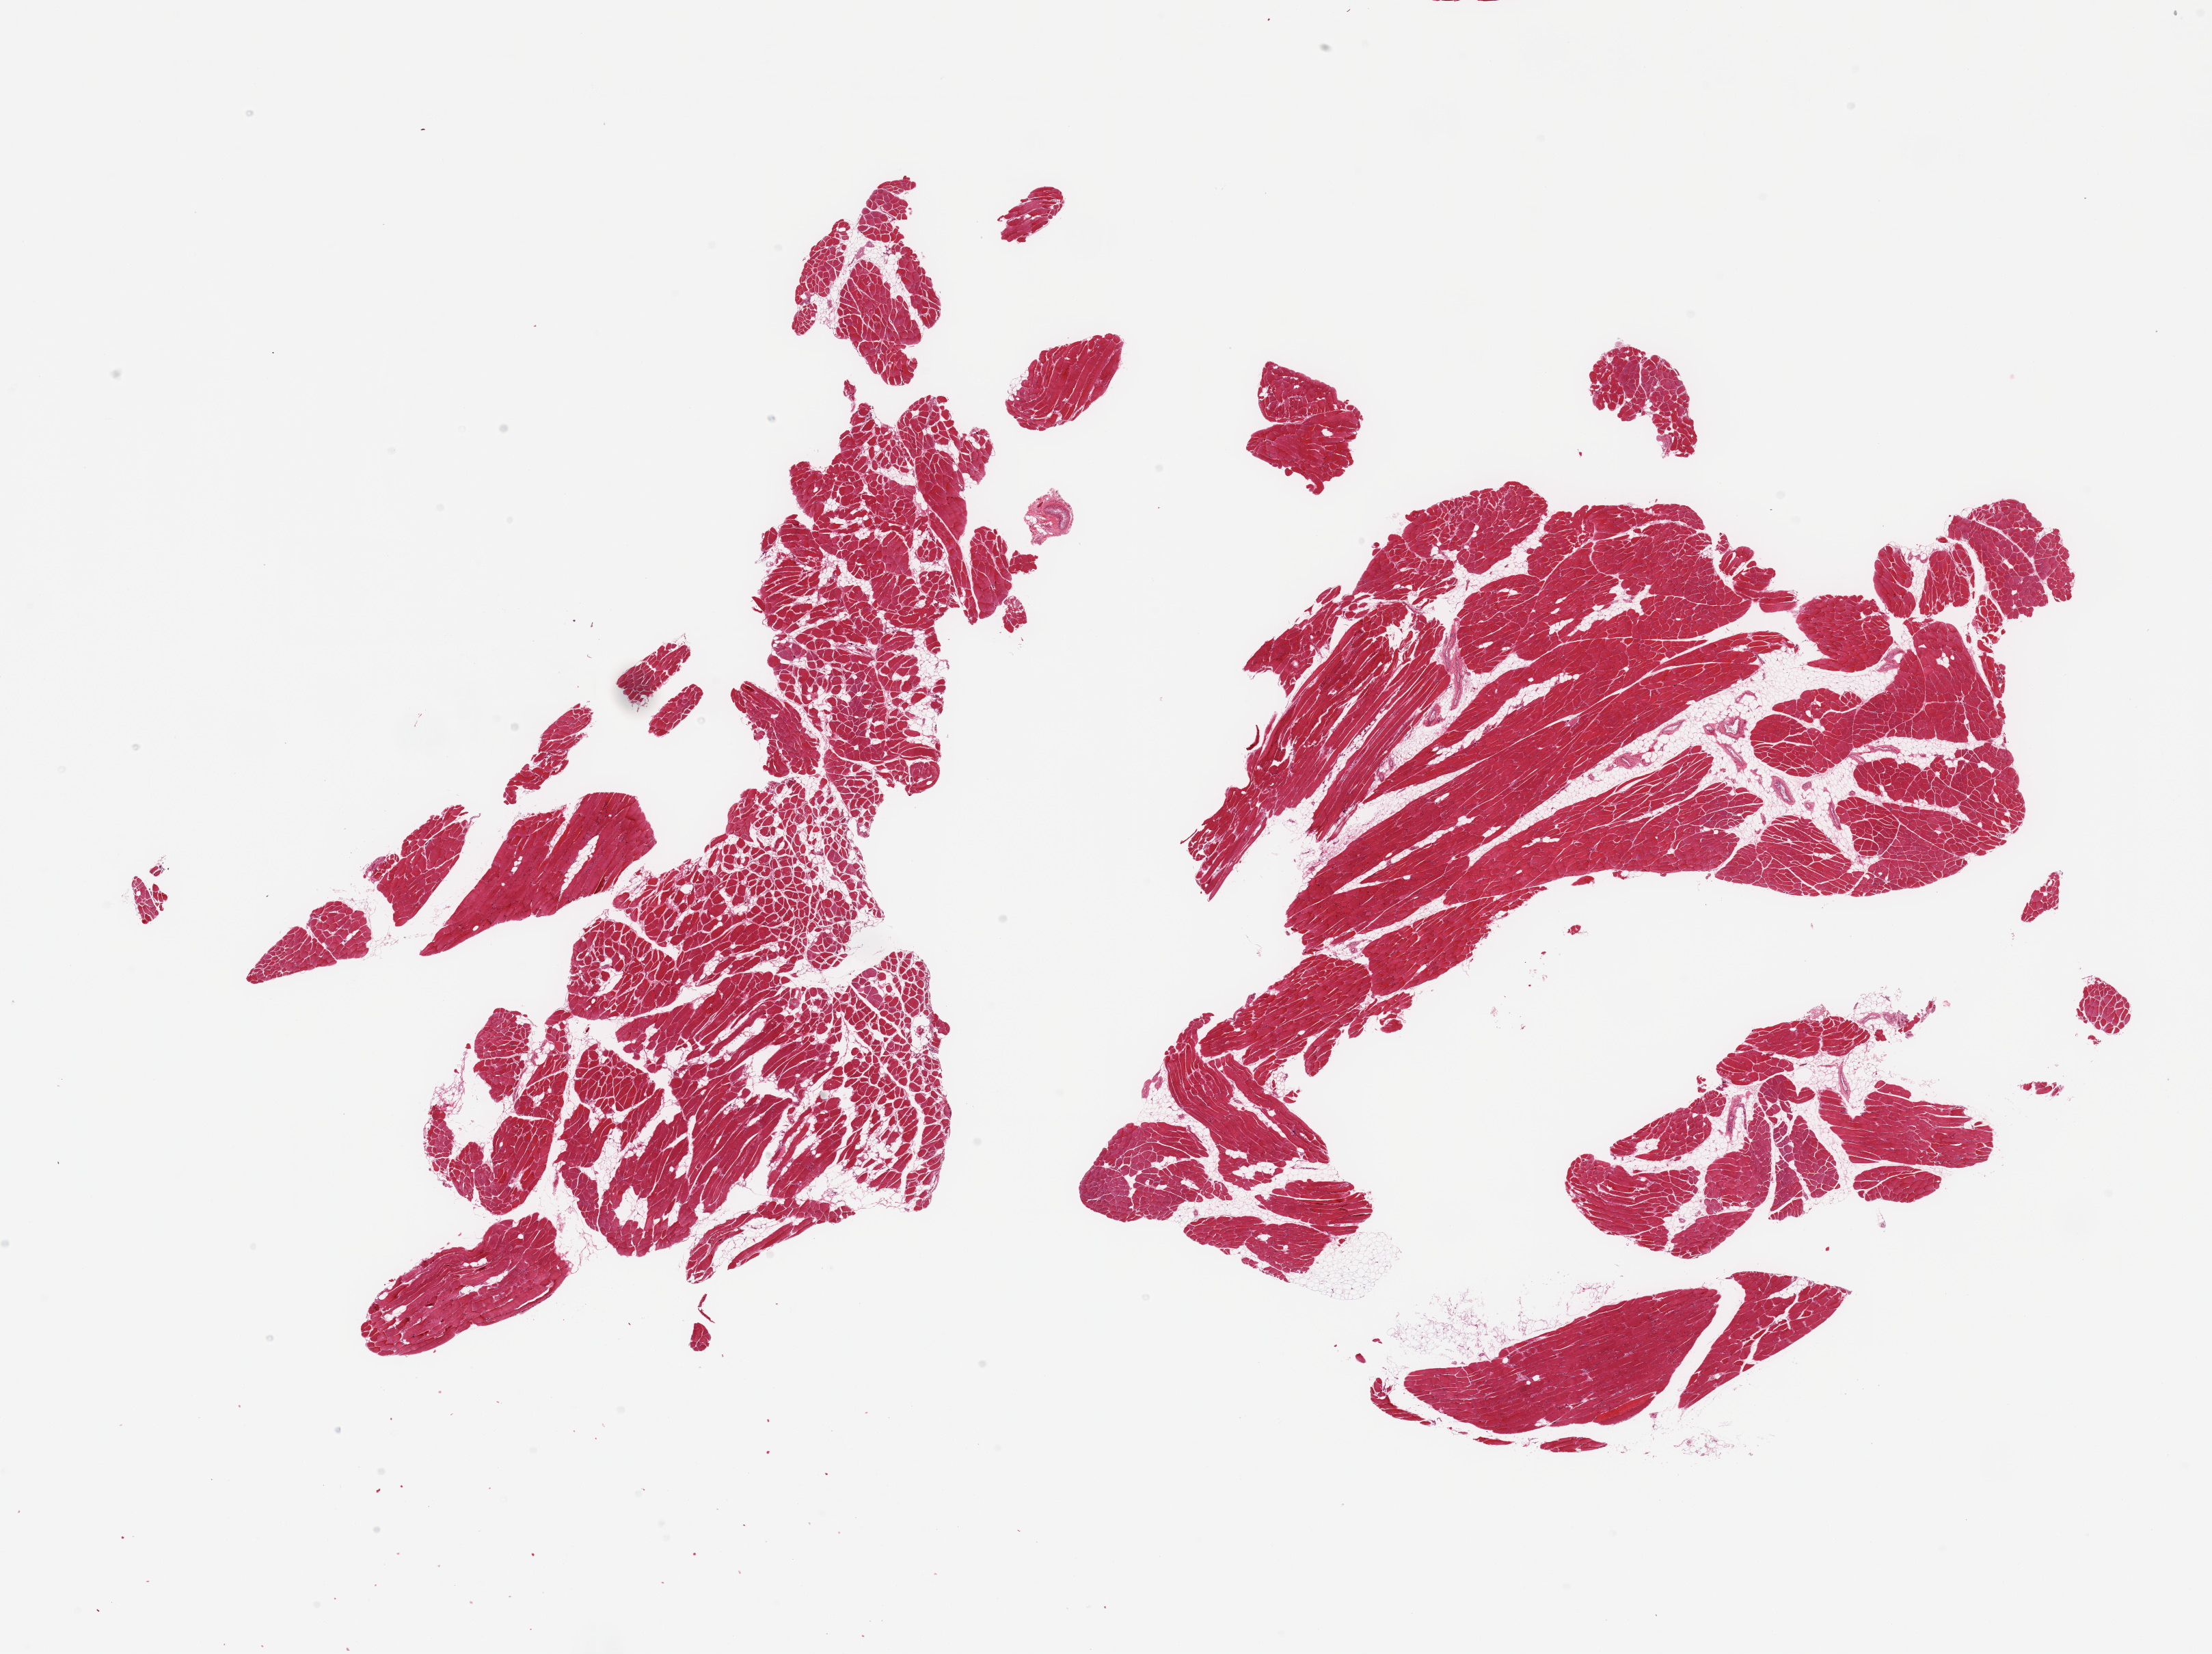
Hematoxylin and eosin (H&E) whole-slide image, brightfield — a low-resolution overview of the entire scanned area, about 25.6 x 19.1 mm, PAXgene-fixed paraffin-embedded (PFPE) section, target tissue: skeletal muscle, tissue donor sample. Donor sex: male.
Pathologist's review note for this sample: 2 fragmented pieces; 10% internal fat.